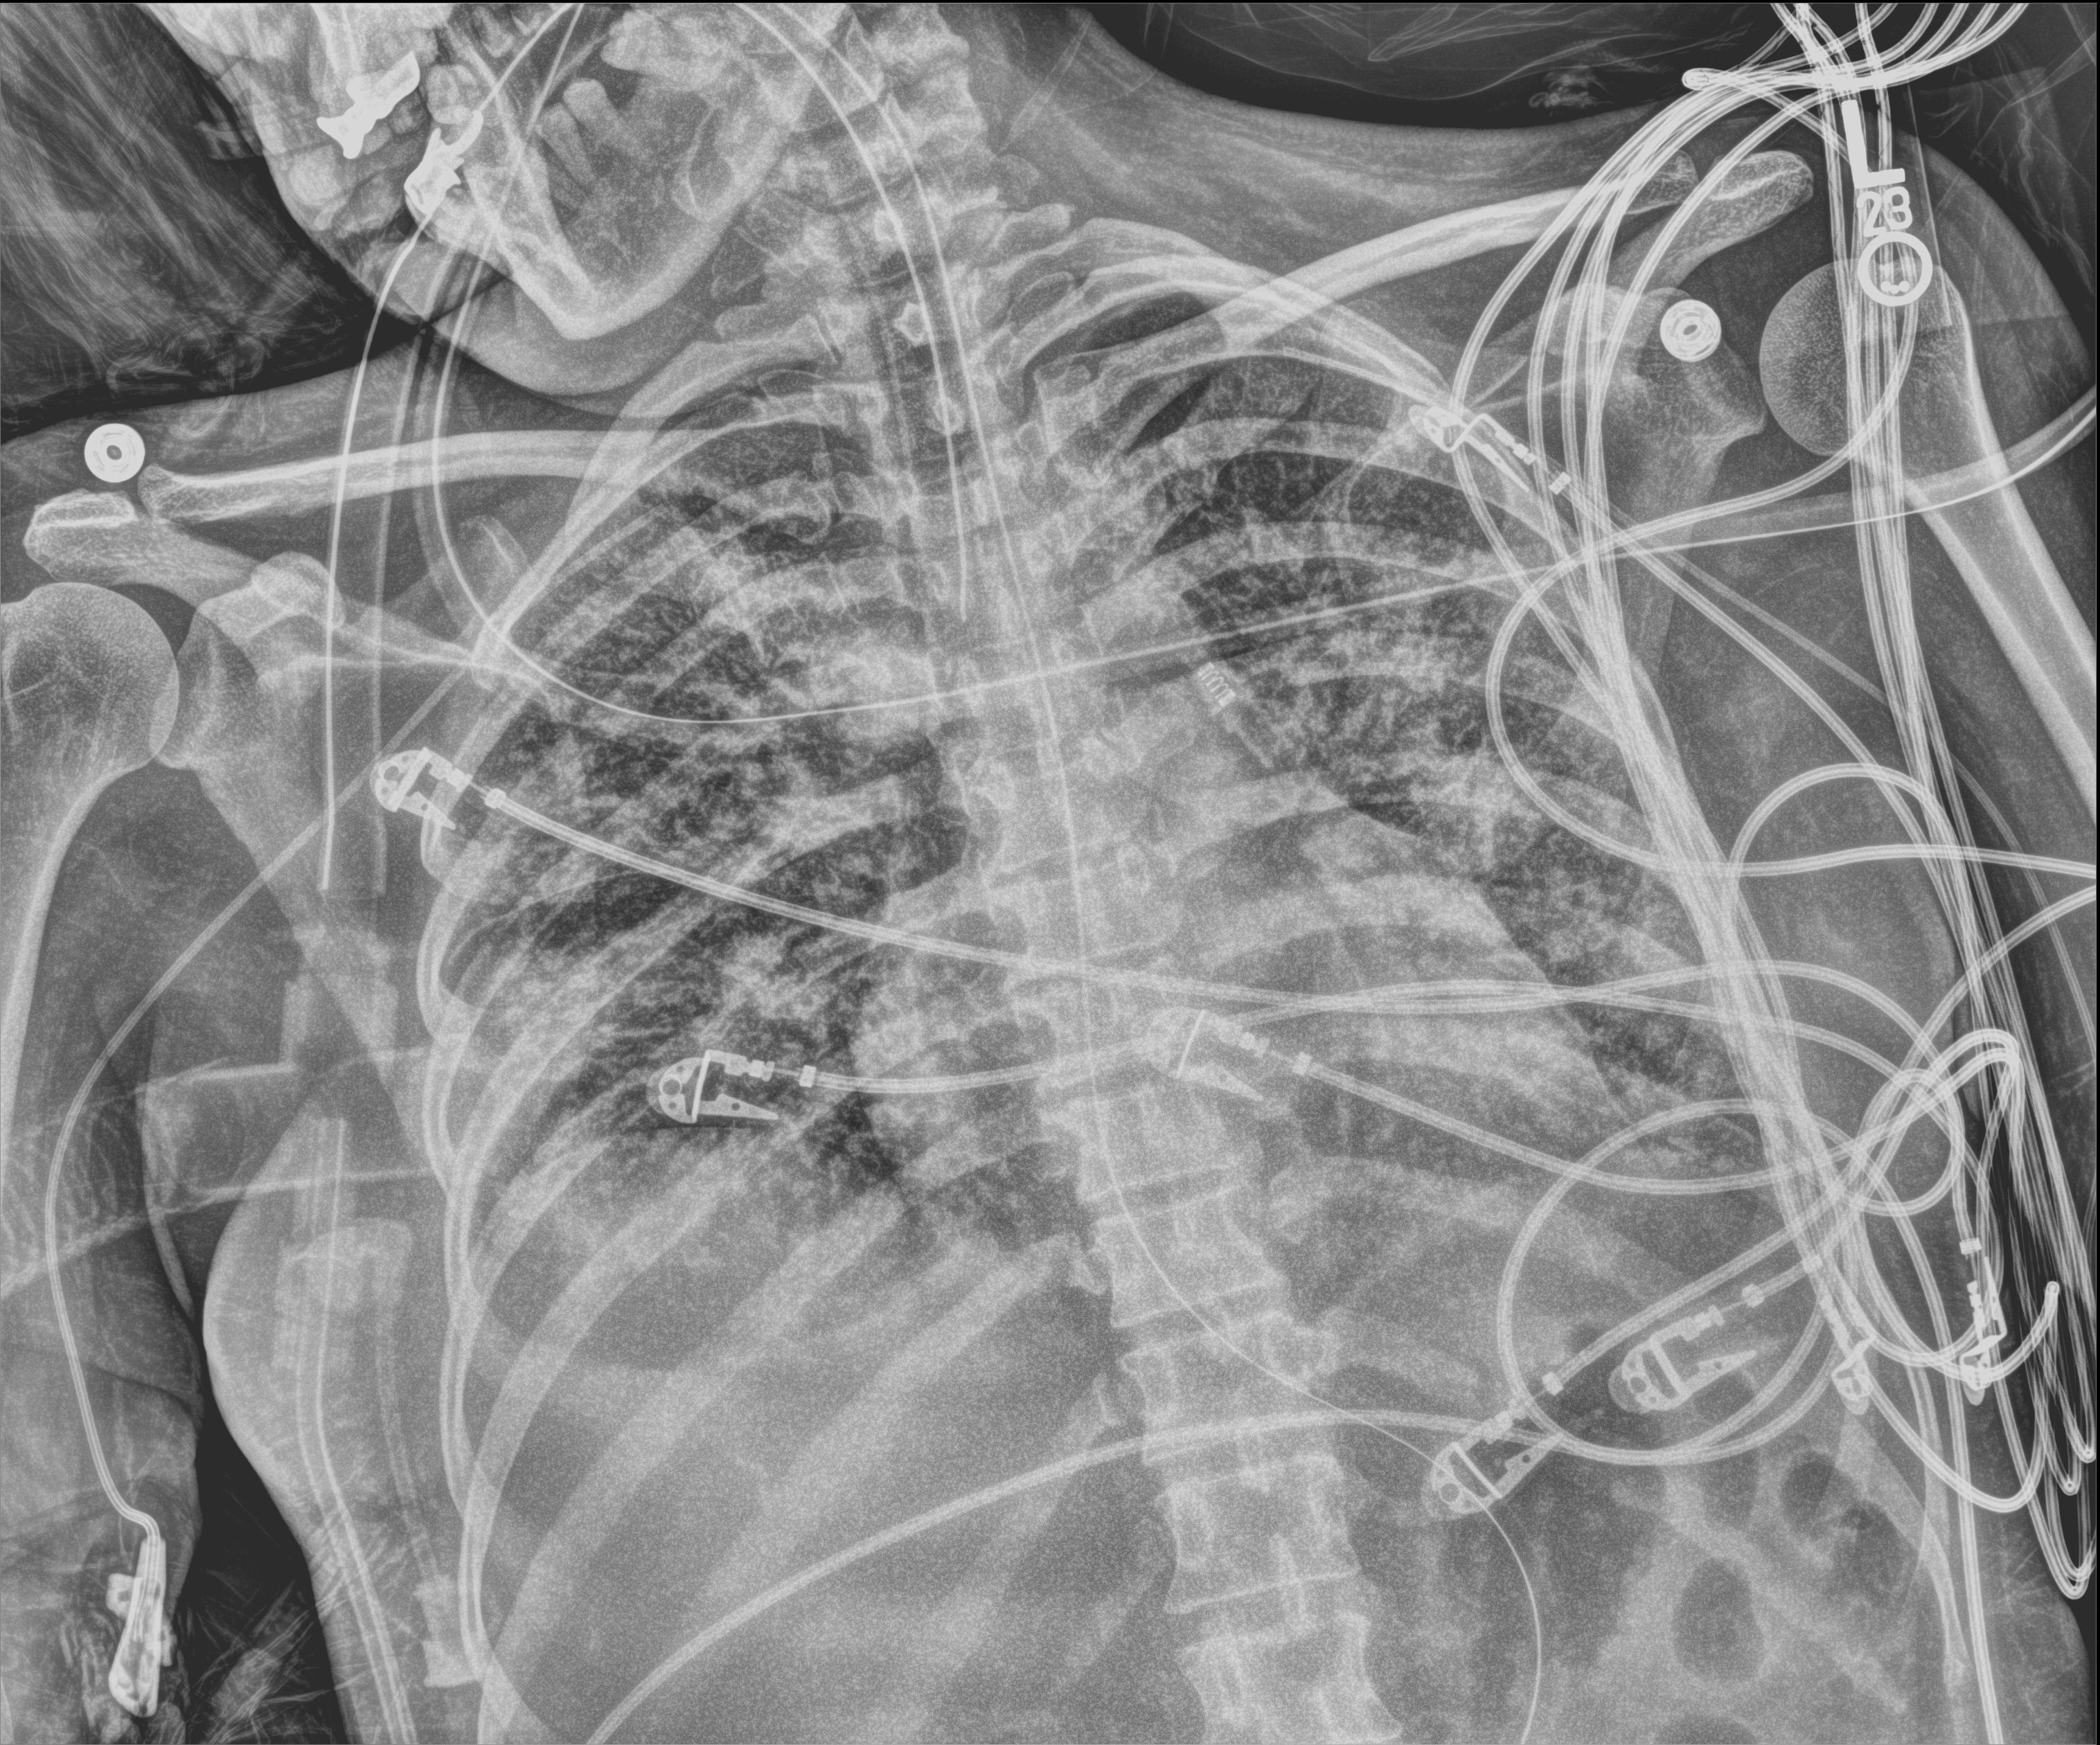
Bedside chest radiograph (digital radiography); anteroposterior (AP) projection. Patient hospitalised with COVID-19; female, aged 18–59 years.
Admission-level facts for this patient (not findings on this image; timing relative to this image not recorded):
- admitted to intensive care during this hospital stay: yes
- mechanically ventilated during this hospital stay: yes